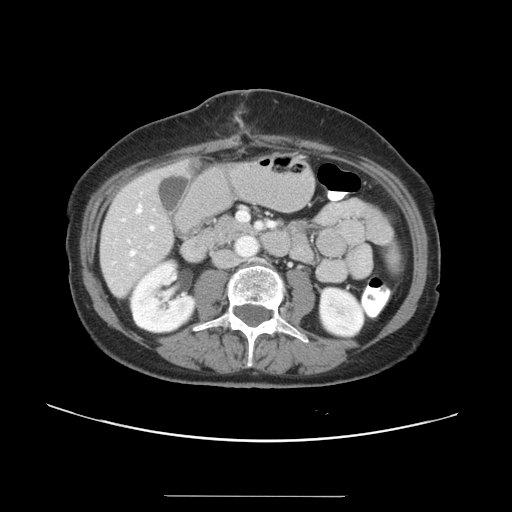
Contrast-enhanced abdominal CT, one axial slice. Position 10 of 34 along the scan axis. 120 kVp. Soft-tissue window (W 400 / L 40 HU). 5 mm slice thickness. 512 × 512 image matrix. Female patient, age 69 years. Case-level facts recorded for this patient, not image findings: diagnosis: colorectal cancer liver metastases, imaged before liver resection; multiple liver metastases: yes; largest metastasis: 1.4 cm.
Annotated regions visible in this slice (manually delineated by an expert):
- hepatic veins: box from (x=122, y=204) to (x=143, y=256) px
- liver: (x=101, y=161)–(x=191, y=297)
- planned liver remnant (the part of the liver to remain after resection): (x=101, y=161)–(x=191, y=297)
- portal vein (with intrahepatic branches): (x=149, y=211)–(x=274, y=230)